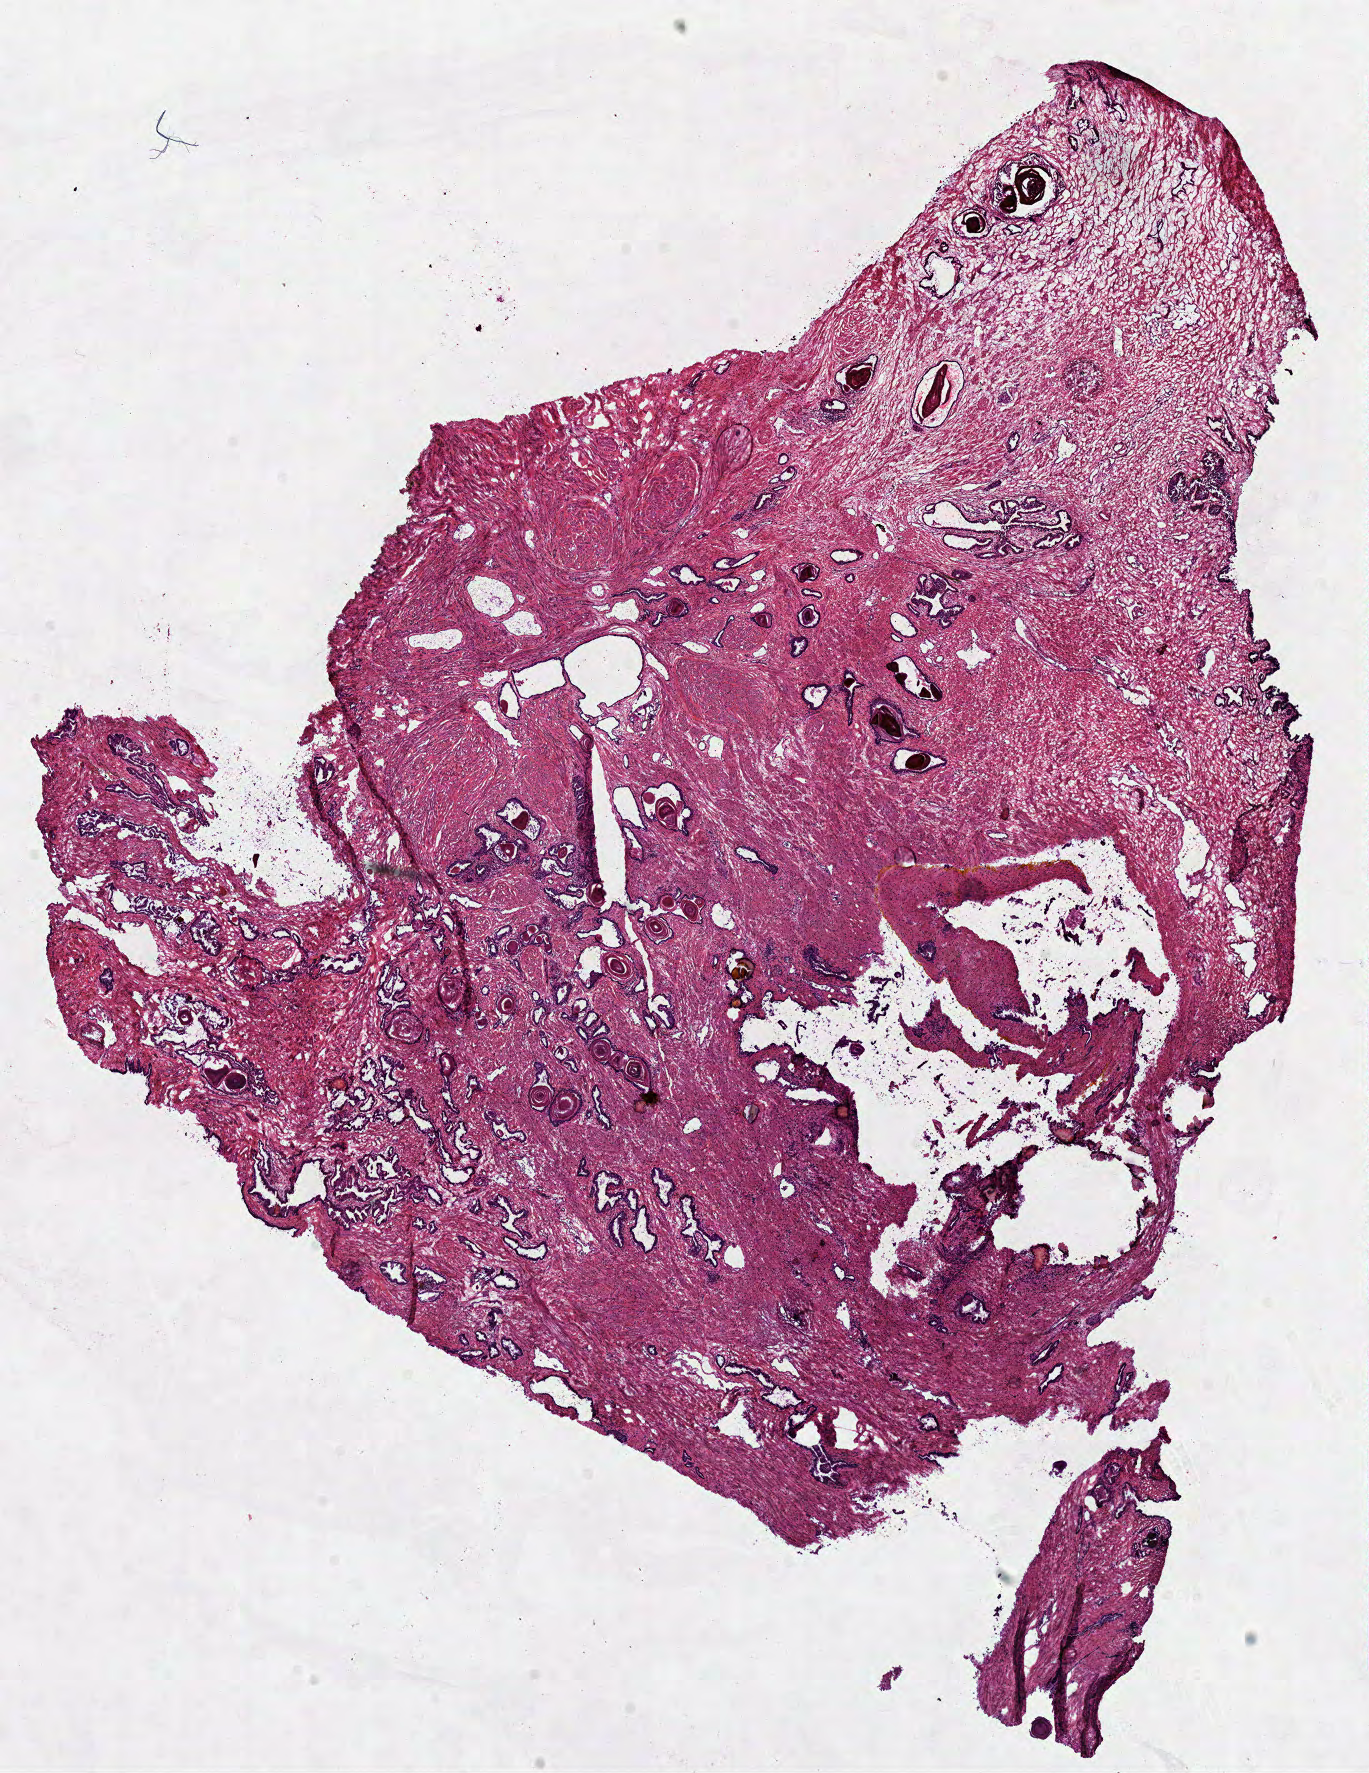
Whole-slide histology image, H&E-stained, a low-resolution overview of the entire scanned area, about 10.8 x 13.9 mm (from a 40x scan). Frozen section. Solid tissue normal (non-tumour tissue) sample from the prostate. Male, age 61 years at initial diagnosis.
This section: solid tissue normal (non-tumour) sample from the same patient. Patient diagnosis: Acinar cell carcinoma (prostate gland).